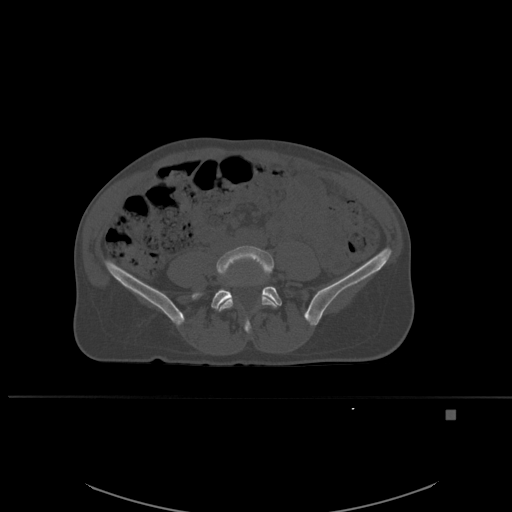
CT including the spine, one axial slice. Slice 181 of 537 in the series (ordered by position). Bone window (W 1800 / L 400 HU). 512 × 512 image matrix, field of view 440 × 440 mm. Patient: female, 45 years. Case-level facts recorded for this patient, not image findings: primary cancer: lung.
Outlined on this slice (semi-automatically segmented with operator editing):
- L4 vertebra: bounding box [x1, y1, x2, y2] px = [214, 246, 277, 334]
- L5 vertebra: [196, 286, 282, 309]